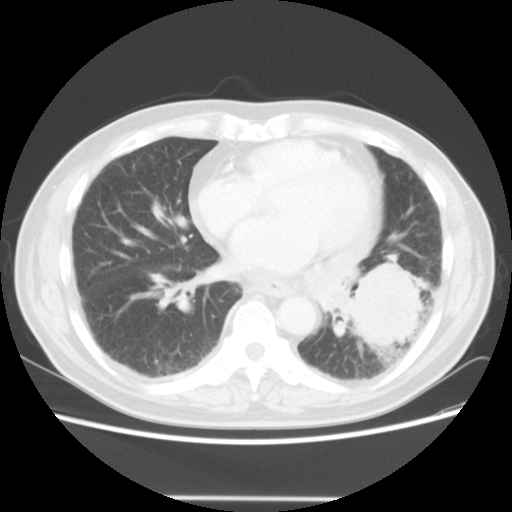
Chest CT, one axial slice. Slice 19 of 56 in the series (ordered by position). Reconstruction kernel STANDARD. Lung window (W 1500 / L -600 HU). 5 mm slice thickness. 512 × 512 image matrix. Patient: male, 66 years. Case-level facts recorded for this patient, not image findings: clinical TNM (as recorded): T4 N3 M0; histopathological grade: G3.
Outlined on this slice (rectangle marked by the reading radiologist):
- lung tumour (recorded histology: small cell carcinoma): bounding box (x1, y1, x2, y2) in pixels: (345, 250, 428, 356)